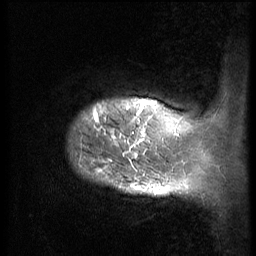
Breast MRI (dynamic contrast-enhanced), one sagittal slice; position 5 of 56 along the scan axis; 3 images stored at this slice position (order not interpretable as contrast timing); 1.5 T; TE 4.2 ms, TR 9 ms; 2.5 mm slice thickness; 256 × 256 image matrix, field of view 180 × 180 mm. Patient: female, 49 years. Case-level facts recorded for this patient, not image findings: setting: breast cancer imaged before/during neoadjuvant chemotherapy; receptor status: HER2-positive.
Annotated regions visible in this slice (semi-automatically segmented with operator editing):
- analysis volume of interest (the breast-tissue region the enhancement analysis was run in; not a lesion): bounding box (x1, y1, x2, y2) in pixels: (65, 85, 168, 207)
- tumour enhancement mask (voxels above the 140 % enhancement threshold inside the analysis volume of interest): (93, 100, 157, 196)